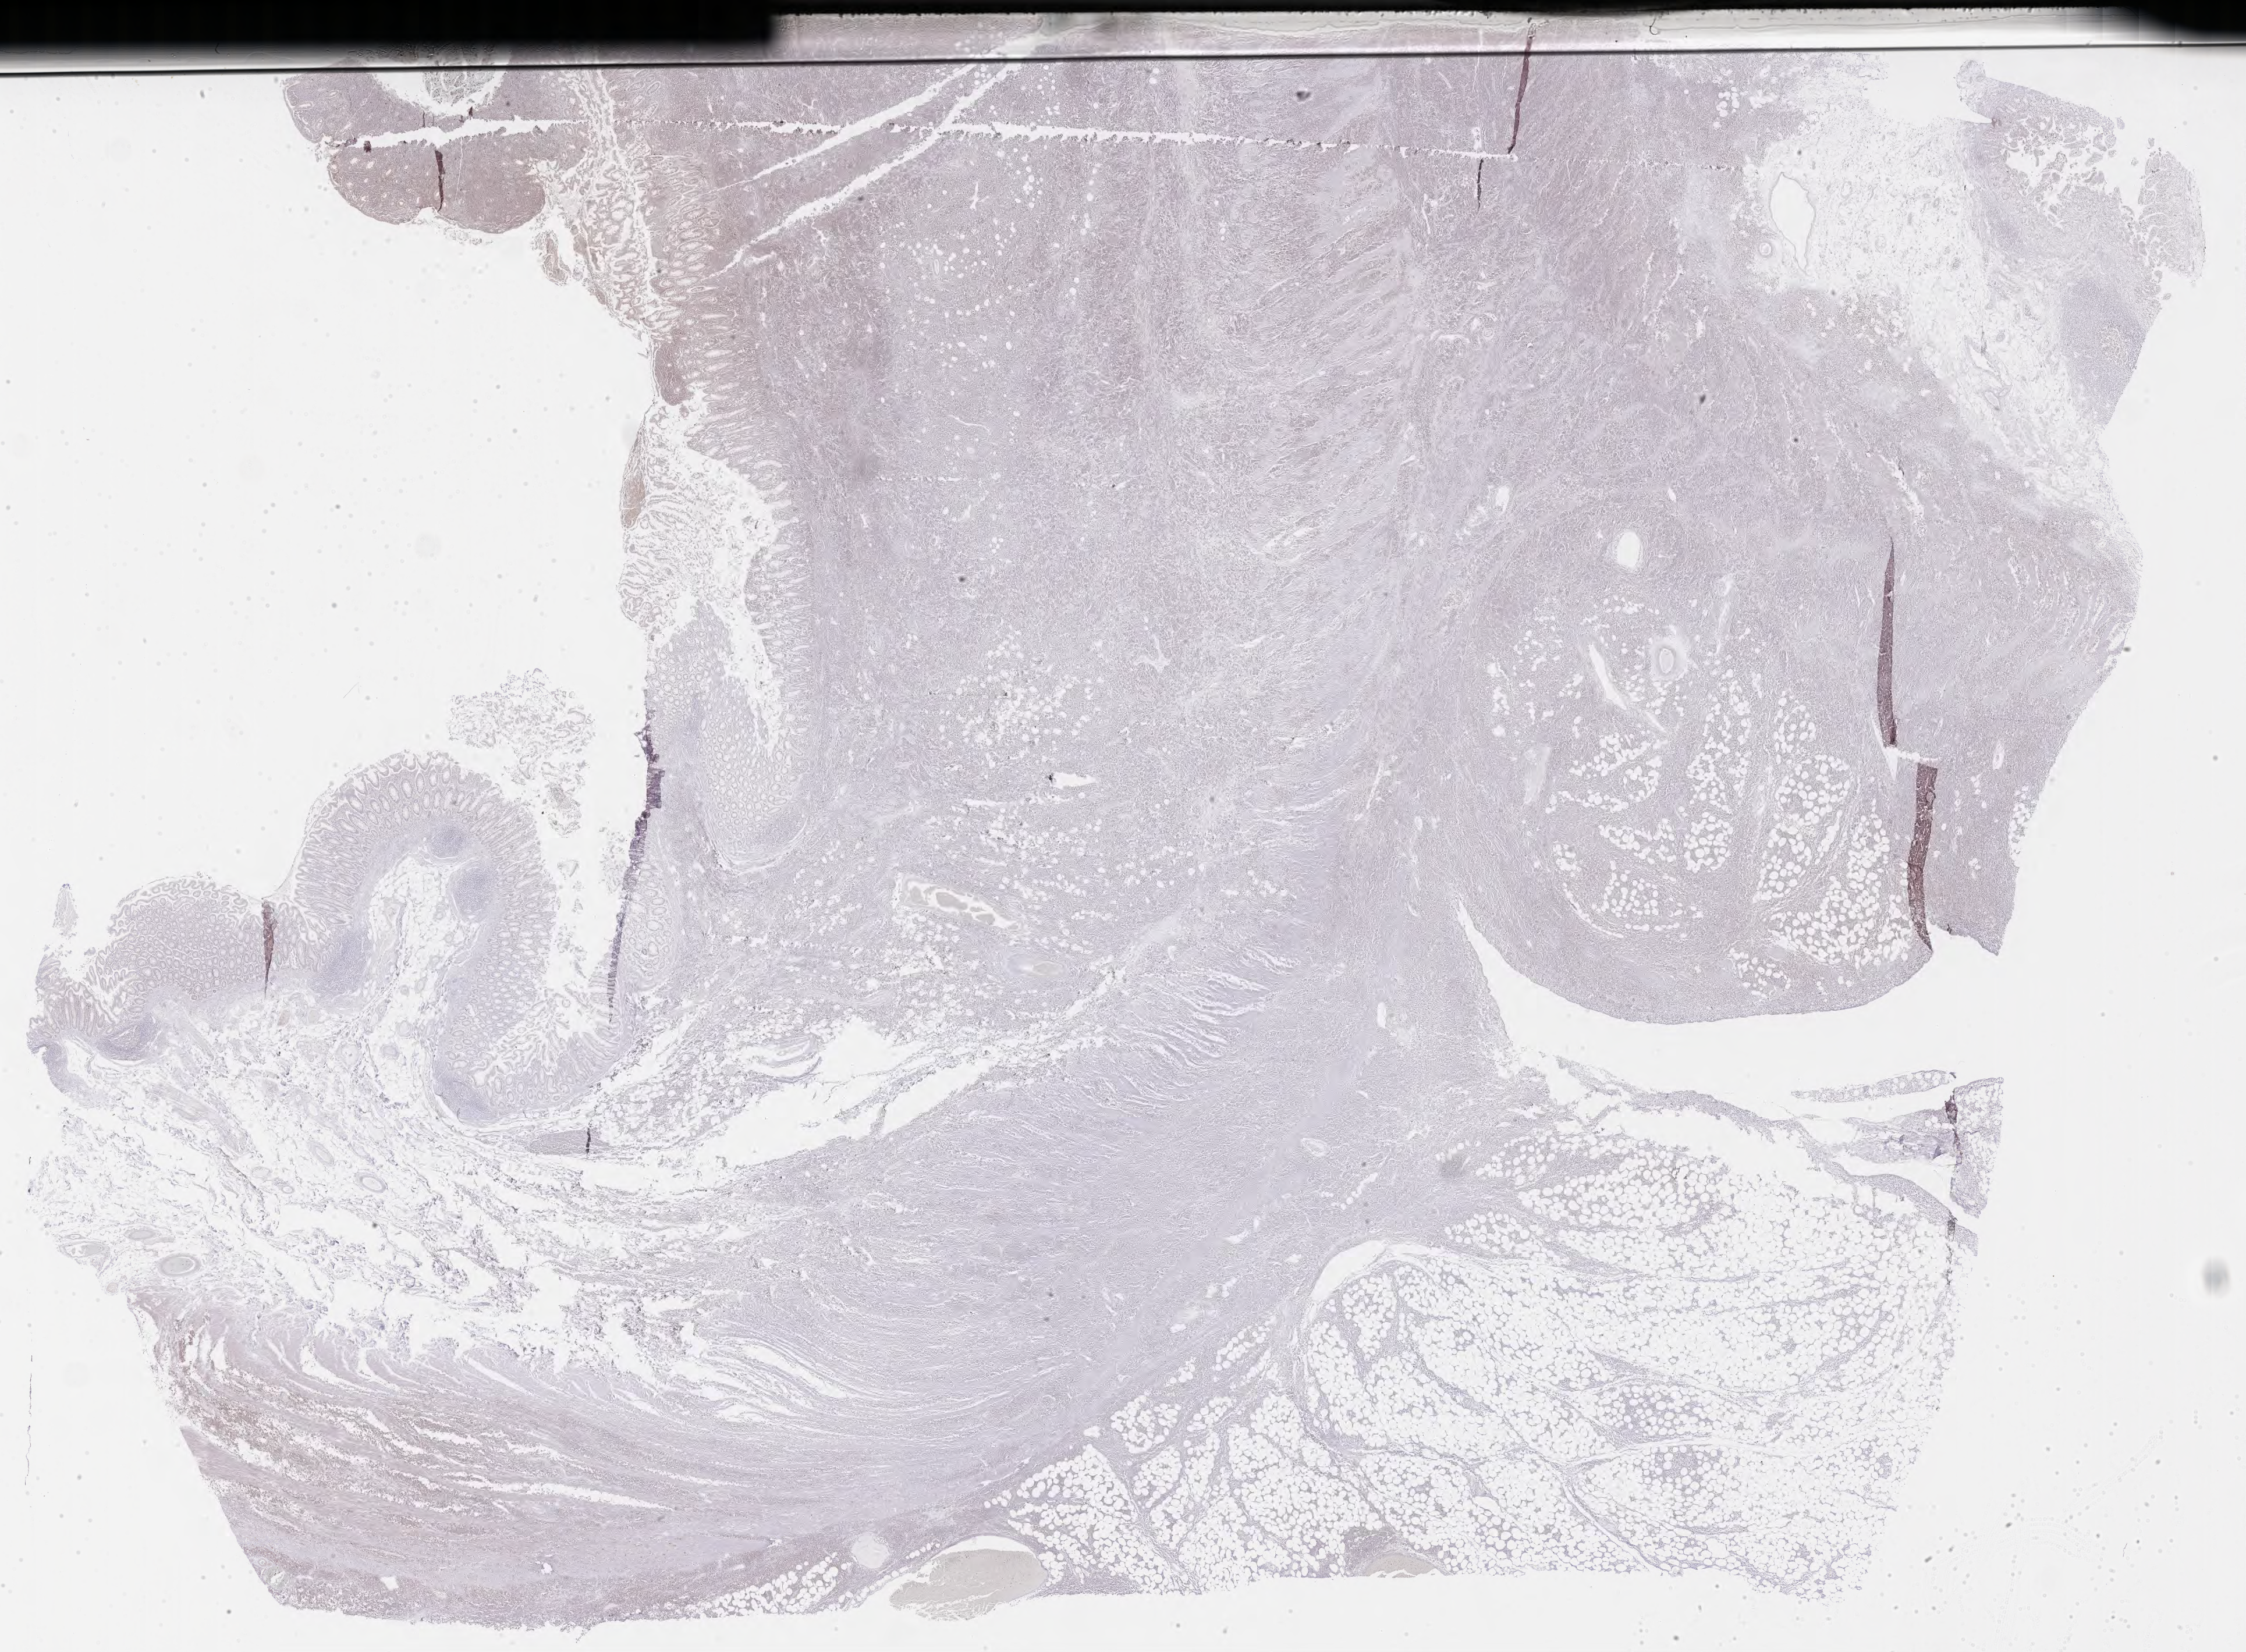
IHC for CD10, whole-slide image — low-resolution overview of the scanned area, about 31.2 x 23.0 mm. Tumor tissue. Patient male; 56 years old.
• histologic diagnosis: Burkitt lymphoma, NOS